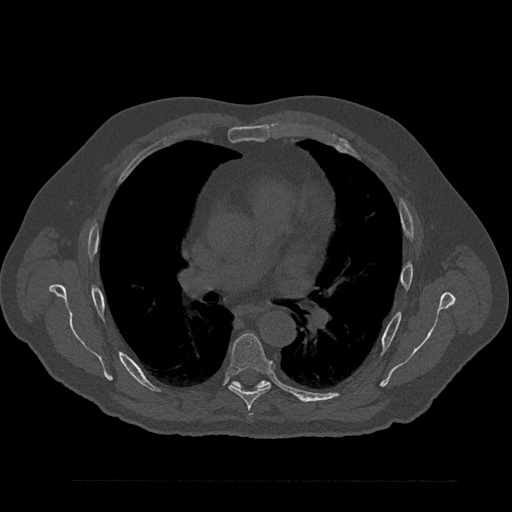
CT including the spine, one axial slice; slice 544 of 797 in the series (ordered by position); 120 kVp; bone window (W 1800 / L 400 HU); 0.5 mm slice thickness; 512 × 512 image matrix. Male patient, age 61 years. From the clinical record (not read from this slice): primary cancer: prostate.
Annotated regions visible in this slice (semi-automatic segmentation, software-assisted and operator-edited):
- T6 vertebra: bounding box <228,333,272,418> (left, top, right, bottom; pixels)
- T7 vertebra: <235,380,269,388>